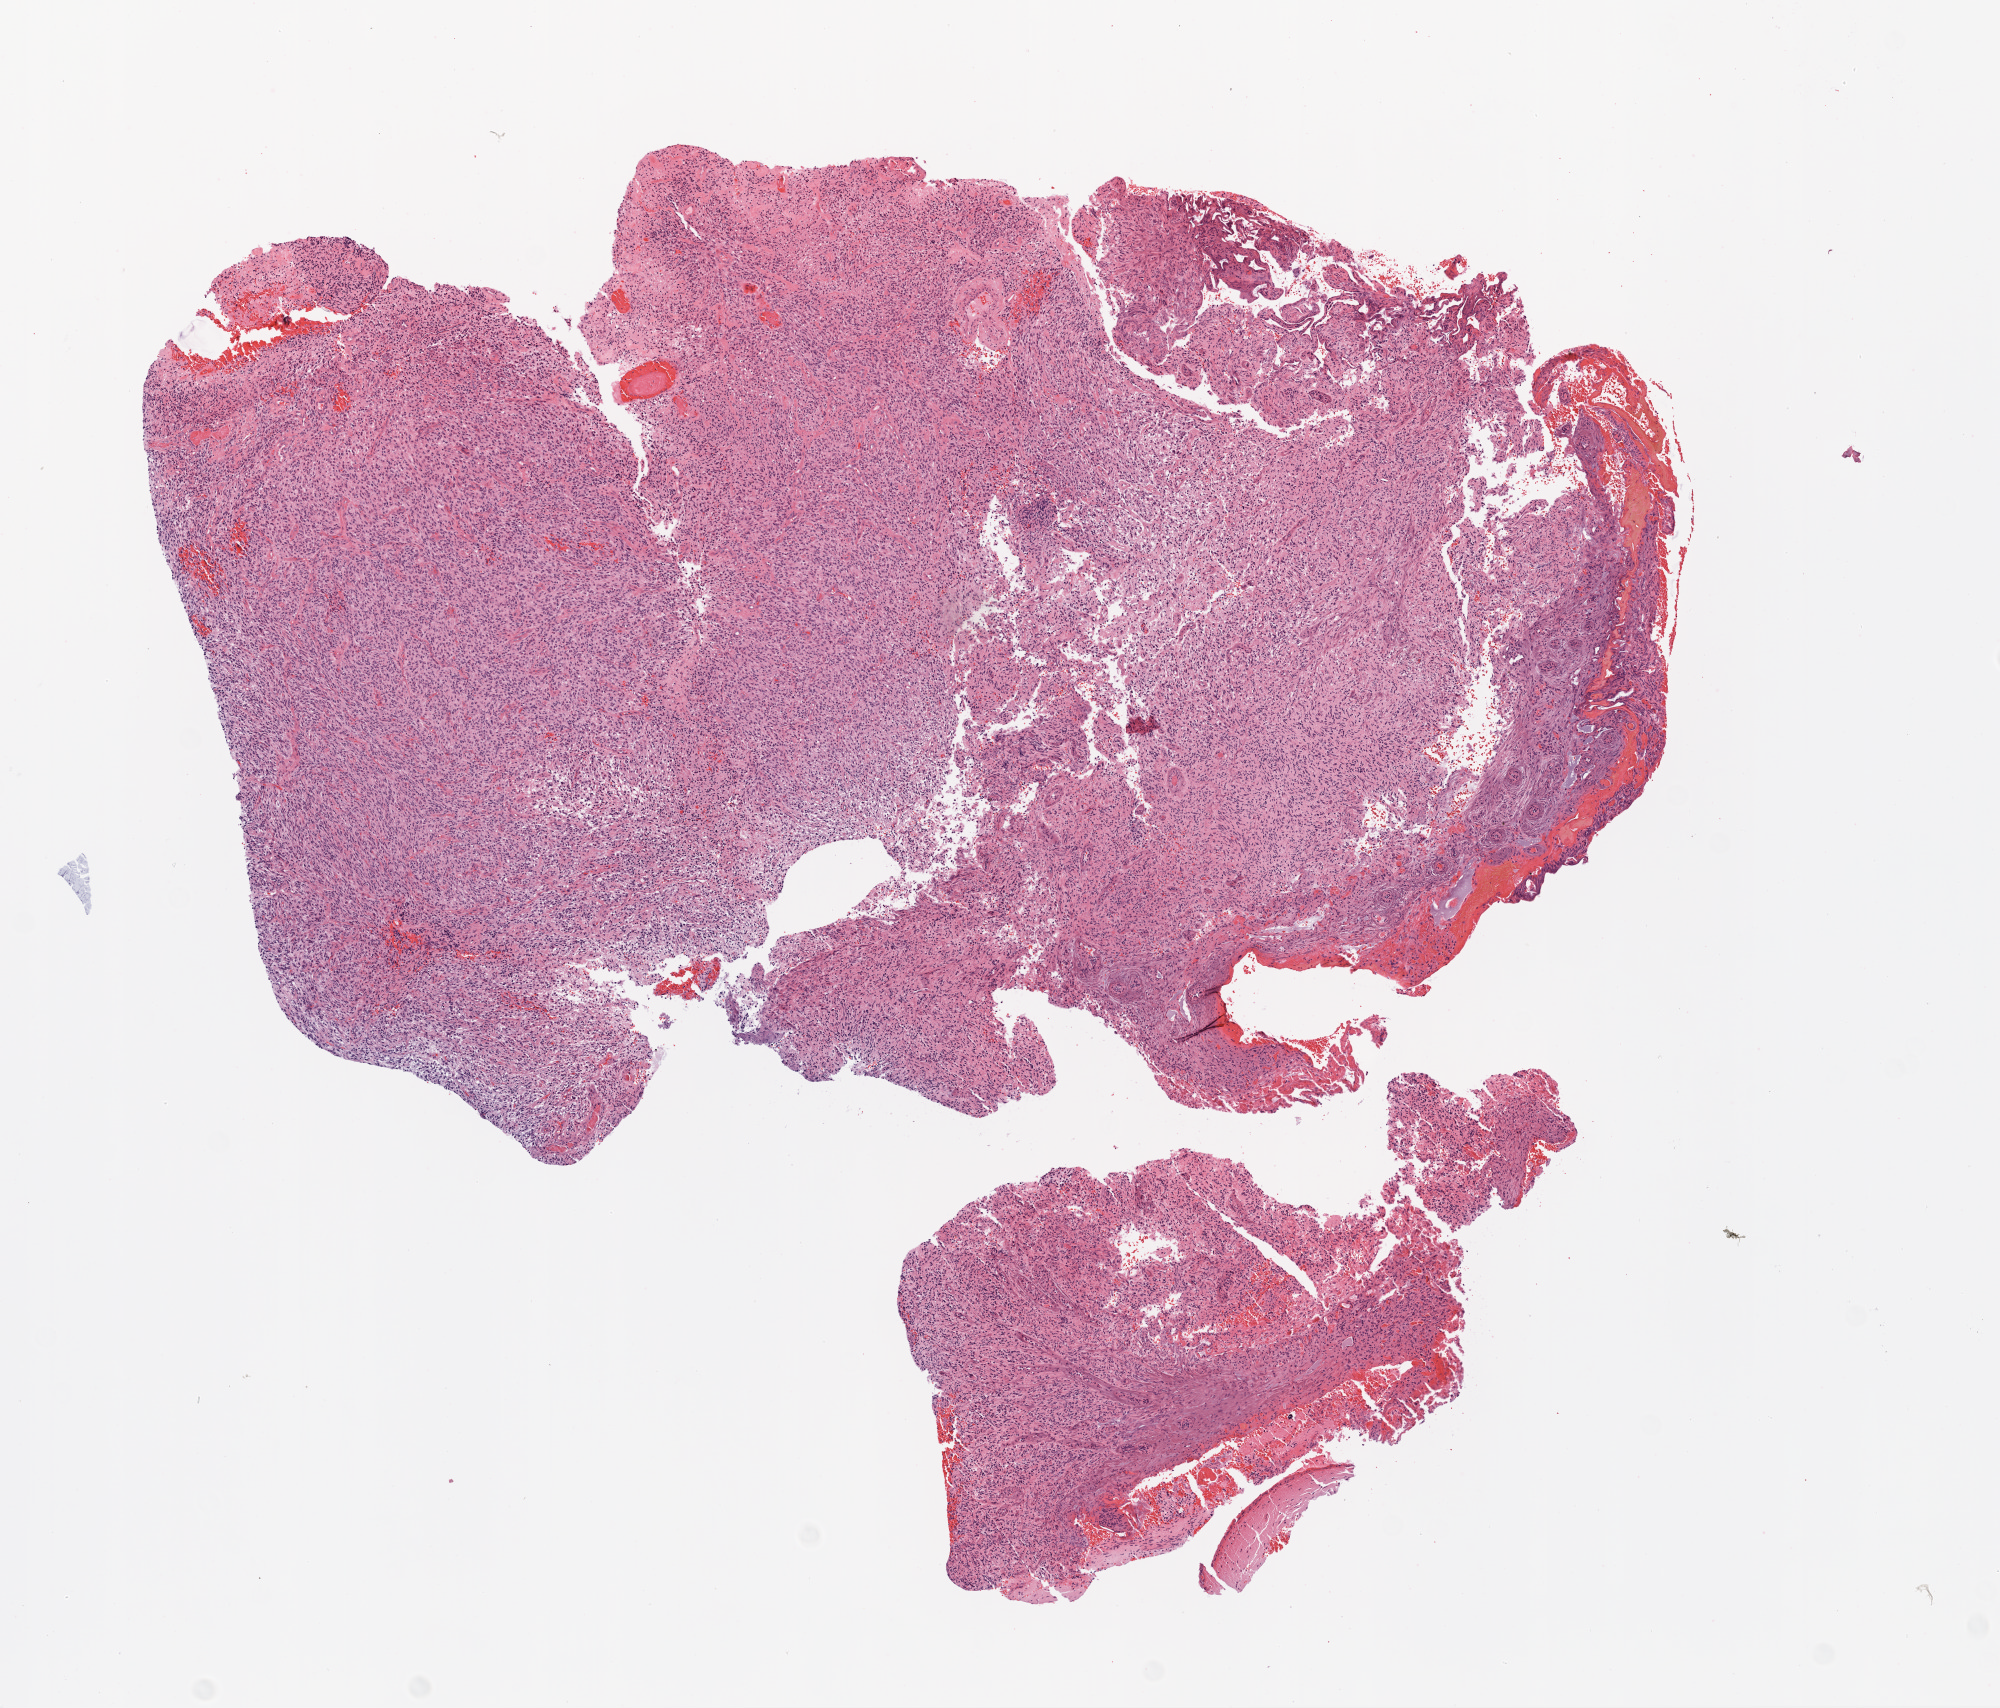
Digitized H&E tissue section (whole slide) — low-resolution overview of the scanned area, about 8.0 x 6.9 mm (slide scanned at 20x), formalin-fixed paraffin-embedded (FFPE) diagnostic section, sample: primary tumour, brain. Patient: female, age at initial diagnosis 63 years.
• diagnosis: Glioblastoma